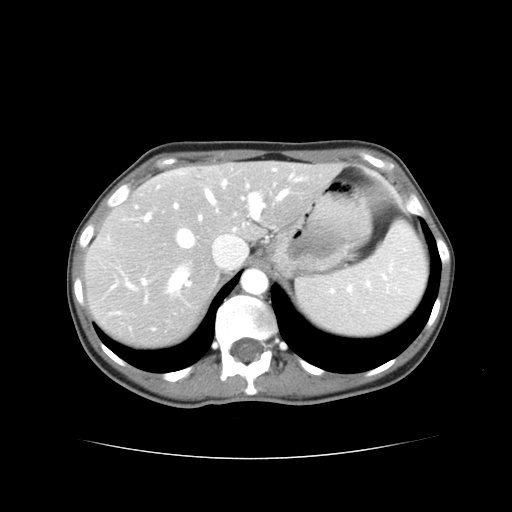
Contrast-enhanced abdominal CT, one axial slice; position 29 of 38 along the scan axis; intravenous contrast given; soft-tissue window (W 400 / L 40 HU); 5 mm slice thickness; 512 × 512 image matrix, field of view 340 × 340 mm. Female patient, age 54 years. Case-level facts recorded for this patient, not image findings: diagnosis: colorectal cancer liver metastases, imaged before liver resection; multiple liver metastases: yes; largest metastasis: 1.1 cm.
Outlined on this slice (manually delineated by an expert):
- hepatic veins: bounding box [x1, y1, x2, y2] px = [169, 191, 287, 291]
- liver: [86, 164, 340, 345]
- planned liver remnant (the part of the liver to remain after resection): [209, 164, 329, 239]
- portal vein (with intrahepatic branches): [143, 193, 265, 284]